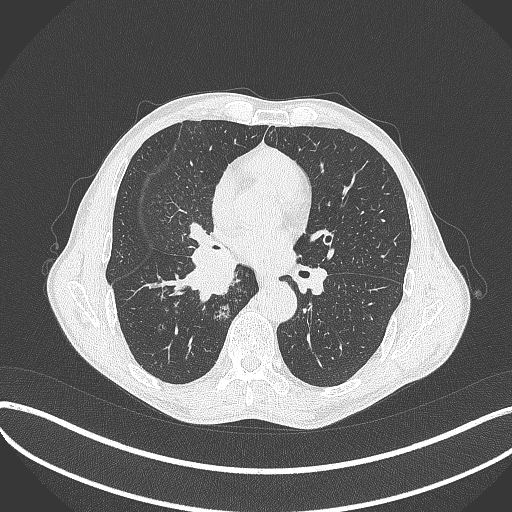
Chest CT, one axial slice; position 220 of 481 along the scan axis; lung window (W 1500 / L -600 HU); 1 mm slice thickness; 512 × 512 image matrix, field of view 400 × 400 mm. Patient: male, 65 years. Case-level facts recorded for this patient, not image findings: clinical TNM (as recorded): T2a N0 M0; histopathological grade: G2.
Structures marked on this image (rectangle marked by the reading radiologist):
- lung tumour (recorded histology: squamous cell carcinoma): bounding box <177,239,243,306> (left, top, right, bottom; pixels)